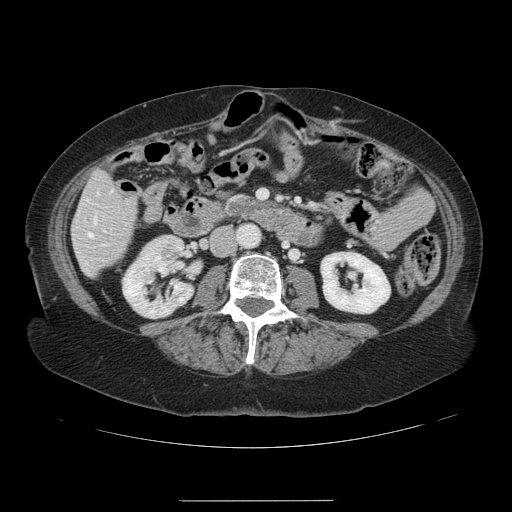
Contrast-enhanced abdominal CT, one axial slice. Position 32 of 141 along the scan axis. 120 kVp. Intravenous contrast given. Soft-tissue window (W 400 / L 40 HU). 2.5 mm slice thickness. 512 × 512 image matrix, field of view 393 × 393 mm. Female patient, age 74 years. From the clinical record (not read from this slice): diagnosis: colorectal cancer liver metastases, imaged before liver resection; multiple liver metastases: yes.
Outlined on this slice (outlined manually by an expert reader):
- hepatic veins: bounding box [x1, y1, x2, y2] px = [89, 217, 96, 236]
- liver: [73, 173, 137, 275]
- planned liver remnant (the part of the liver to remain after resection): [77, 173, 130, 275]